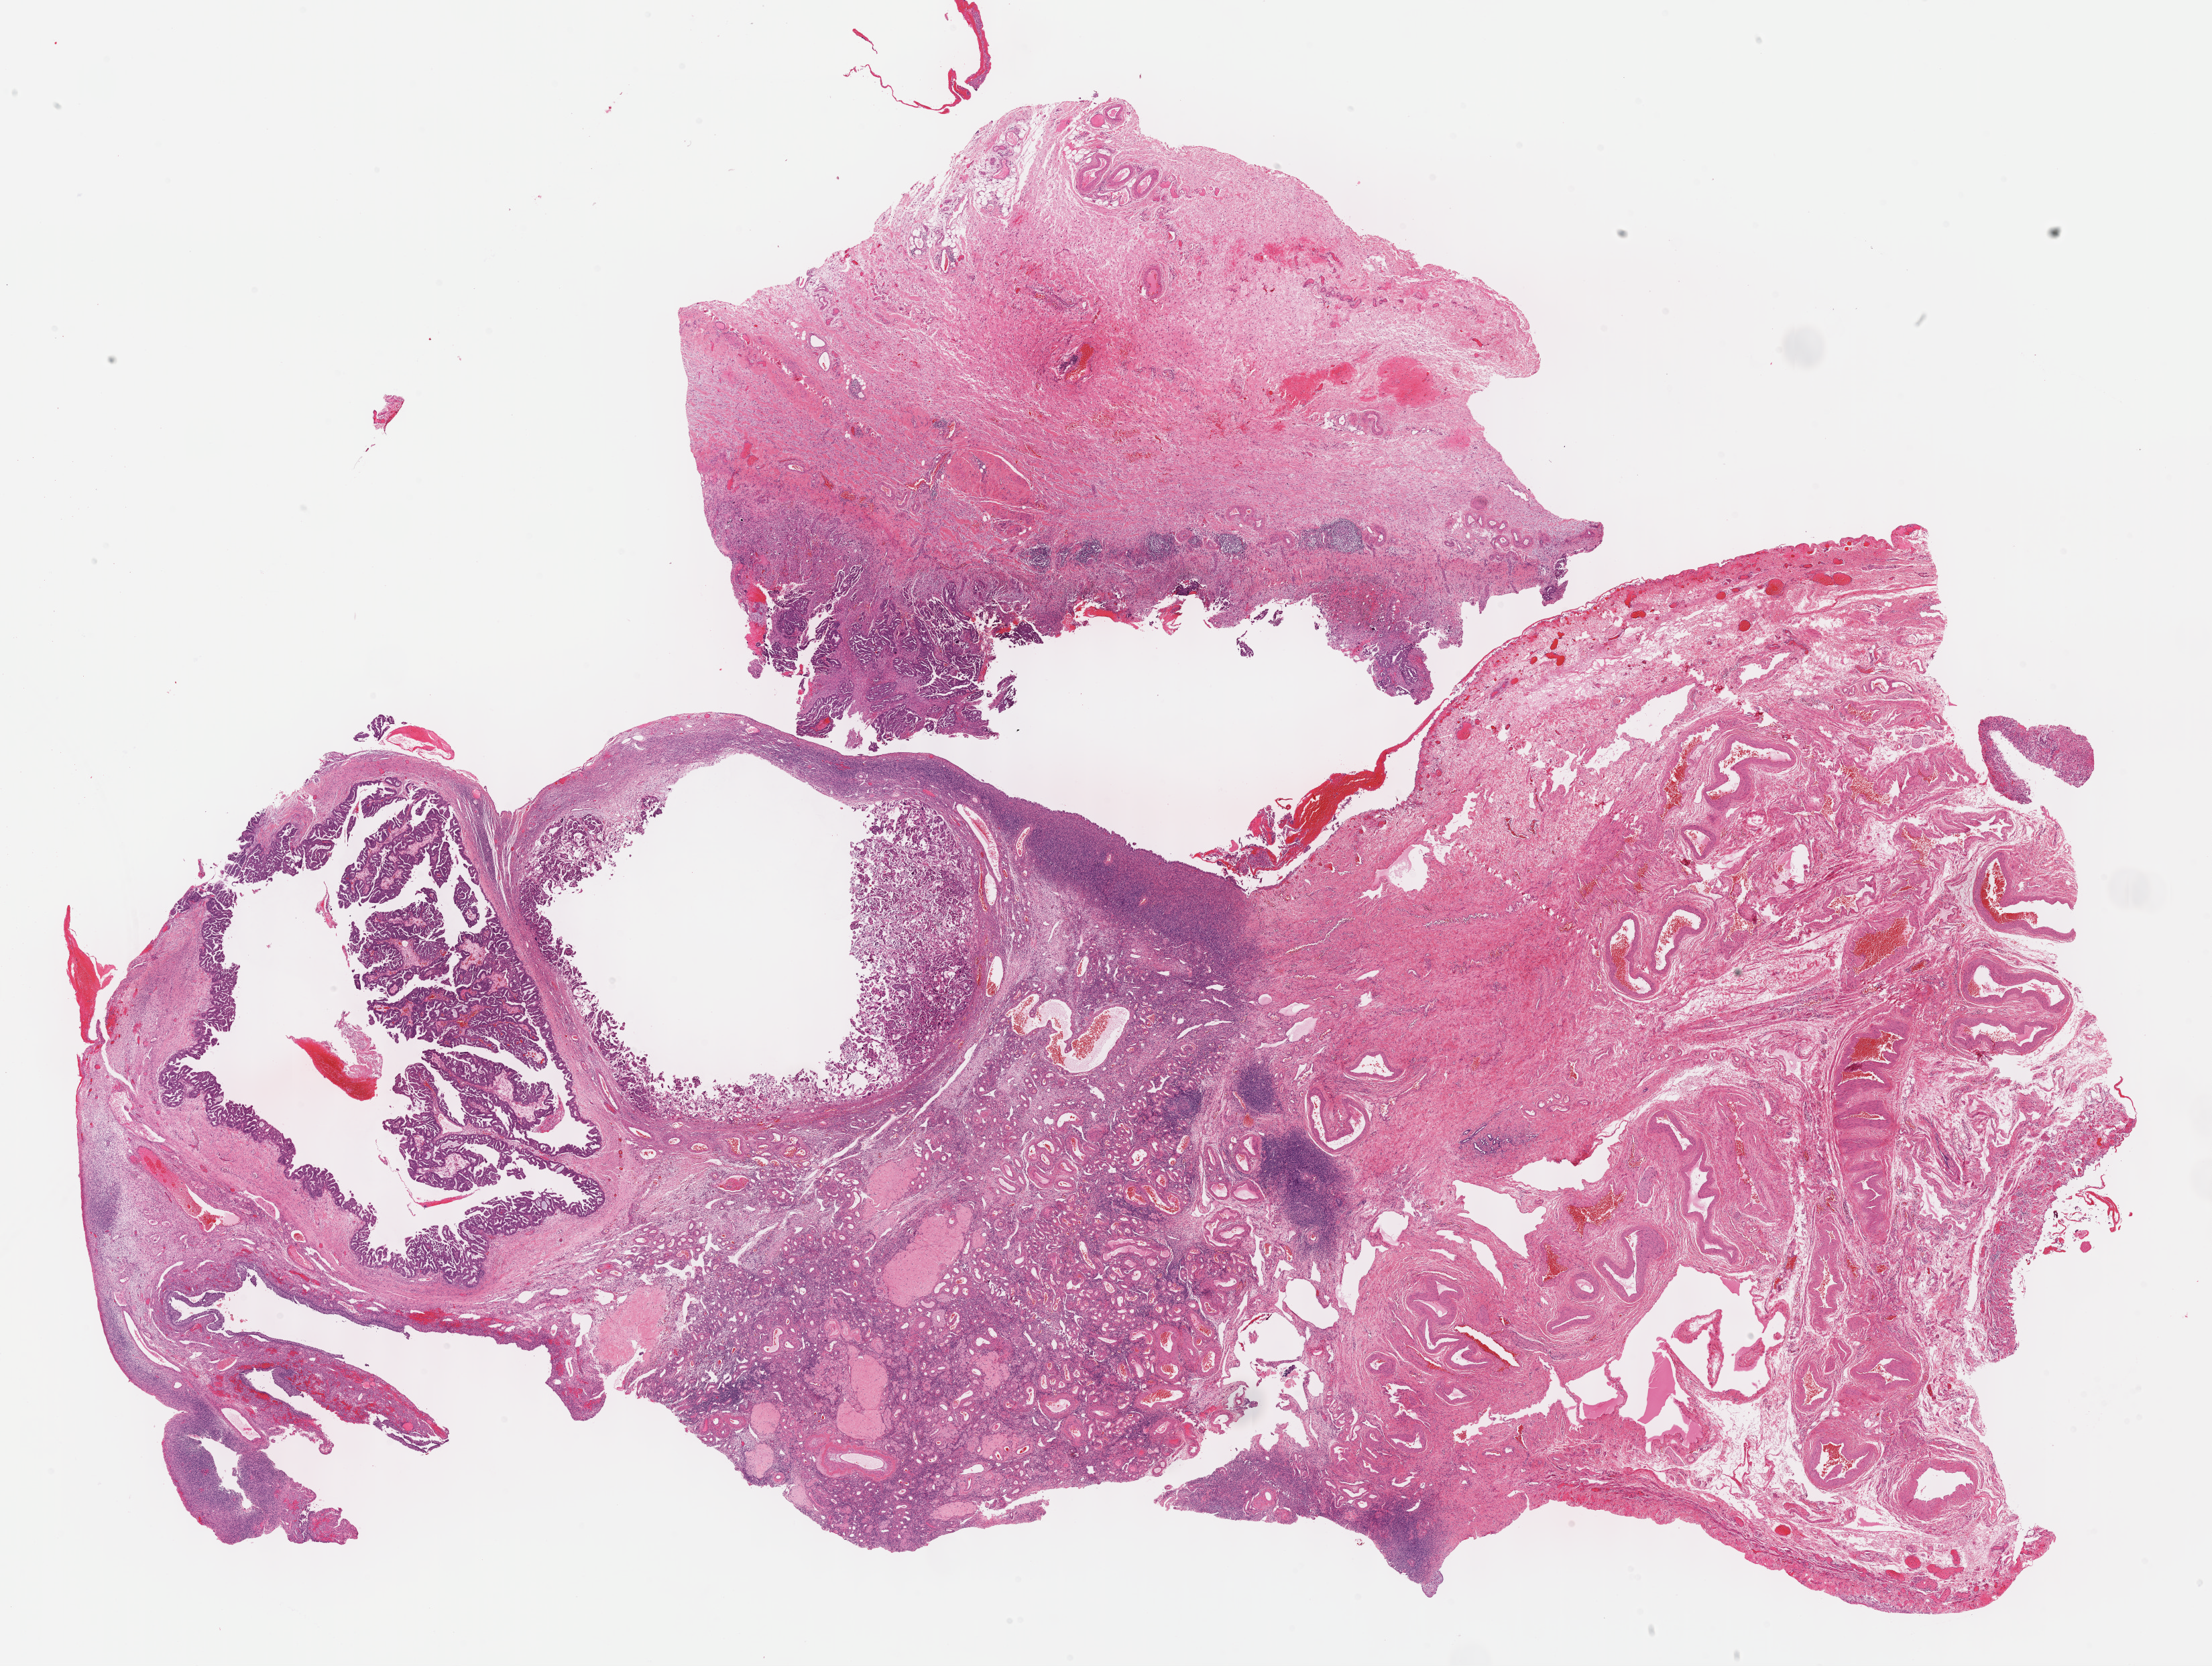
H&E whole-slide image — whole scanned area (about 26.7 x 20.1 mm) shown as a low-resolution overview. Formalin-fixed paraffin-embedded (FFPE) diagnostic section. Sample: primary tumour, ovary. Patient: female, age at initial diagnosis 49 years.
Diagnosis: Serous cystadenocarcinoma, NOS.